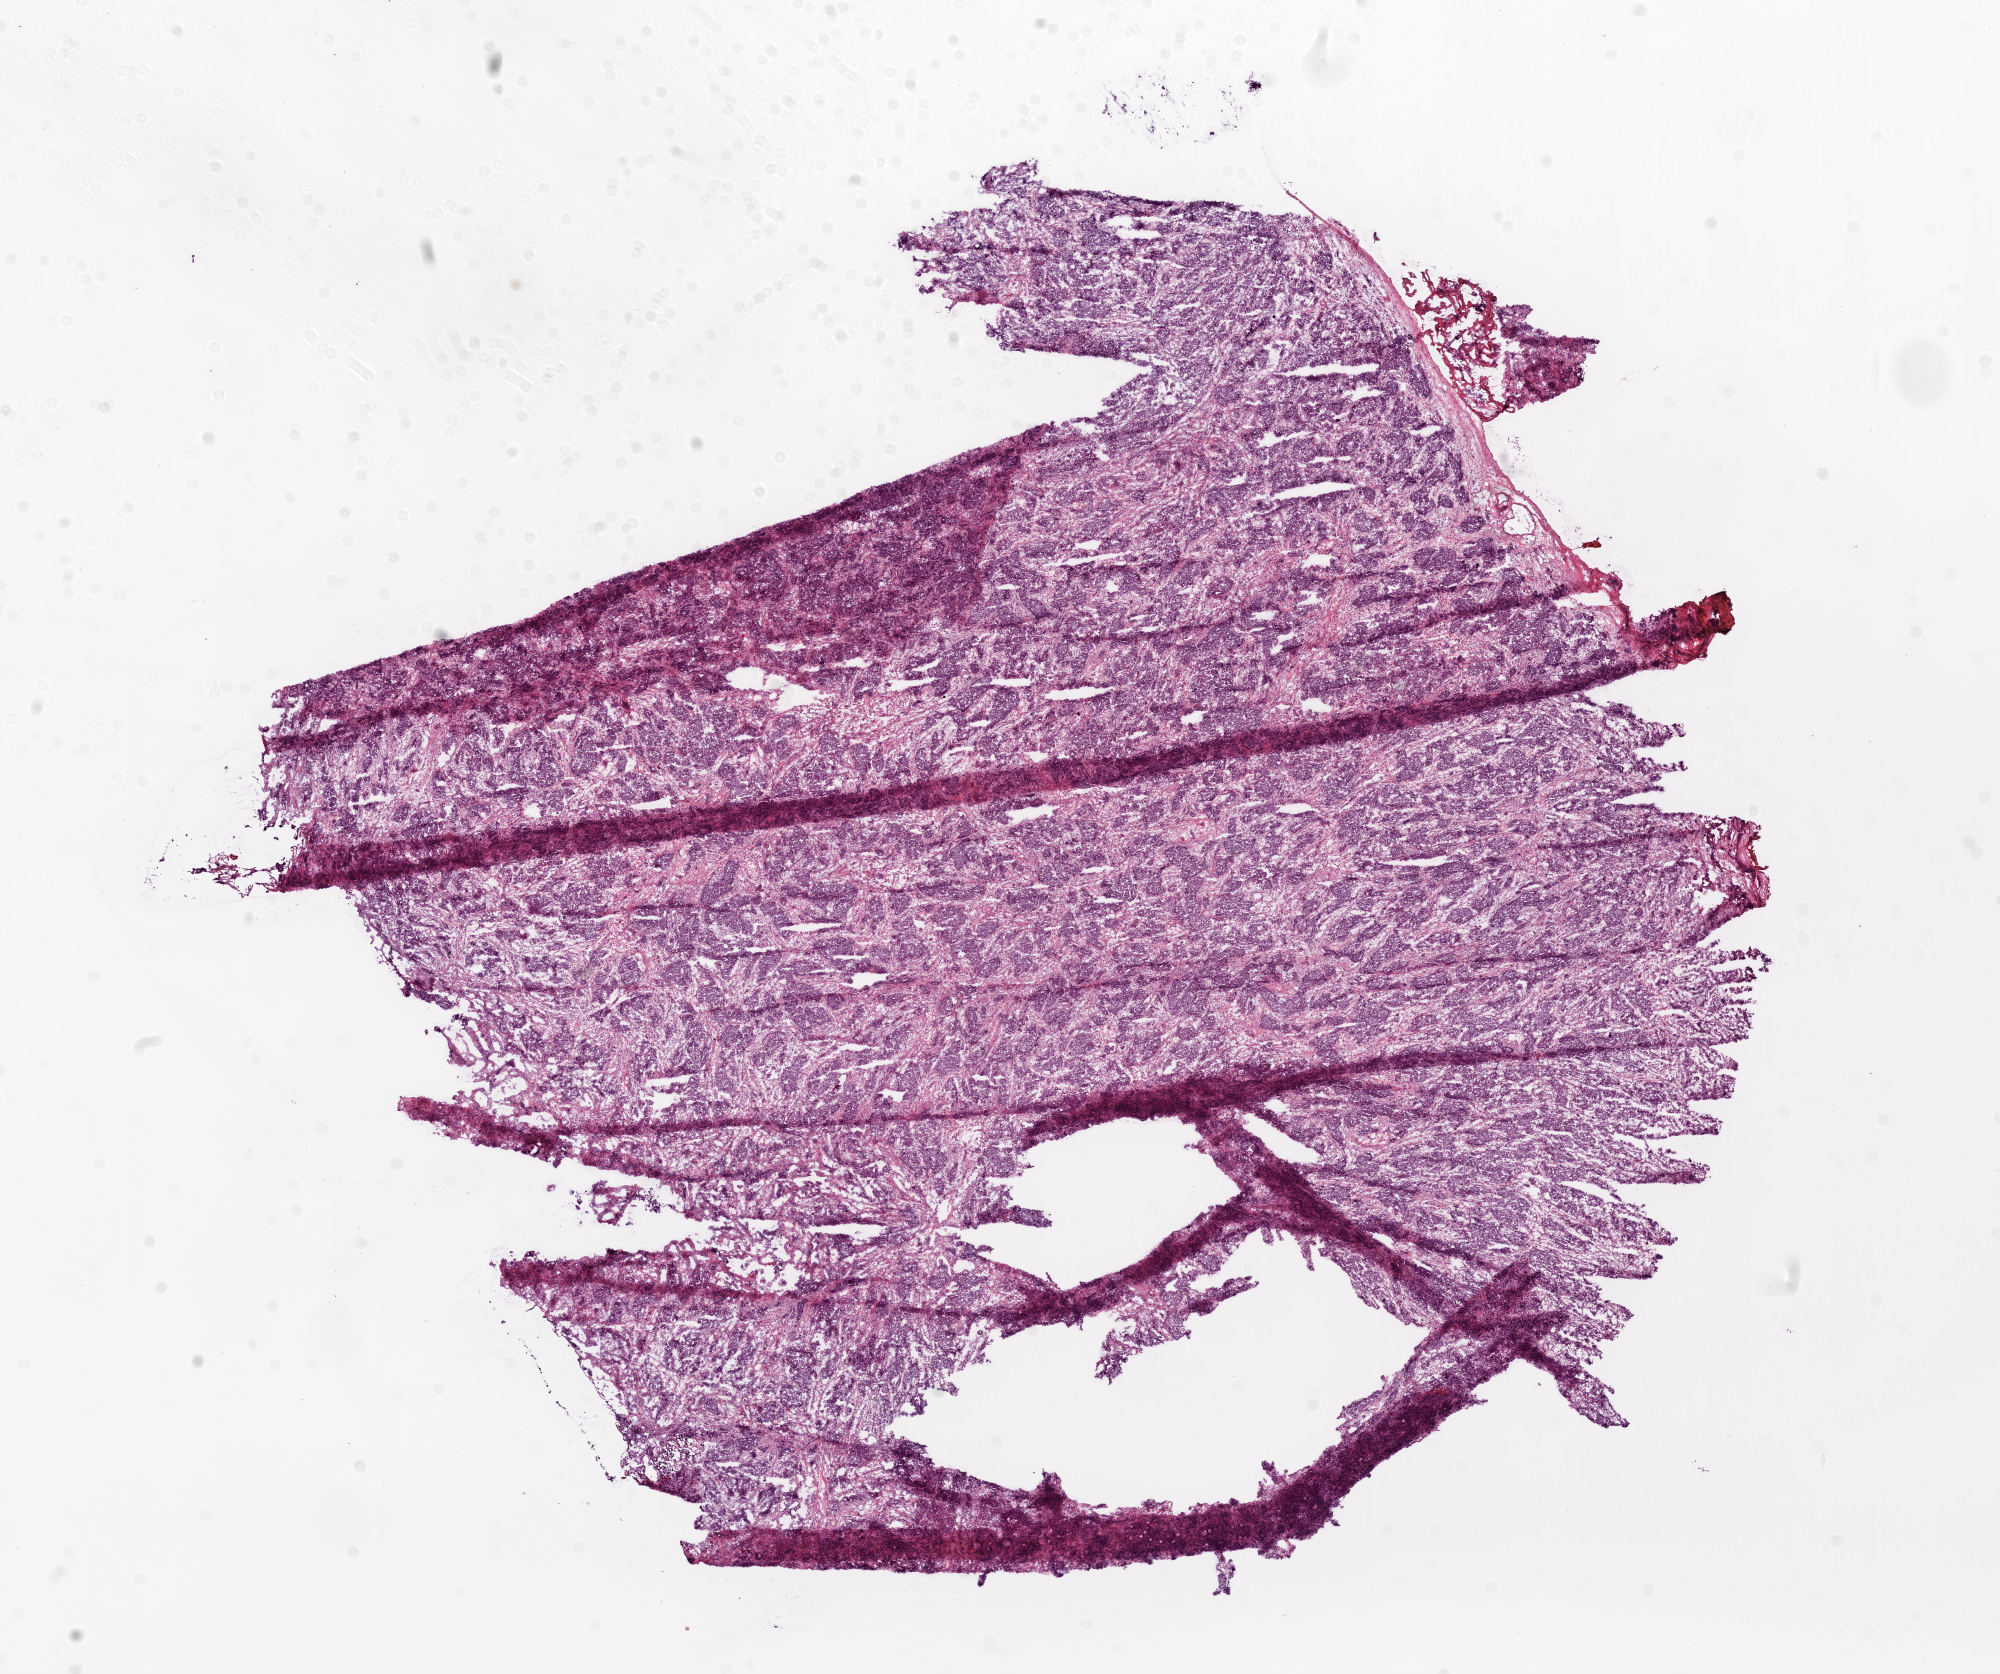
Whole-slide histology image, H&E — a low-resolution overview of the entire scanned area, about 16.0 x 13.4 mm (from a 20x scan). Frozen section. Sample: primary tumour, ovary. Patient: female, age at initial diagnosis 68 years. Histologic grade: G3 (poorly differentiated). Slide review estimates, as recorded: tumour cells 89%, tumour nuclei 90%, normal cells 0%, stromal cells 10%, necrosis 1%.
* FIGO stage: IV
* diagnosis: Serous cystadenocarcinoma, NOS